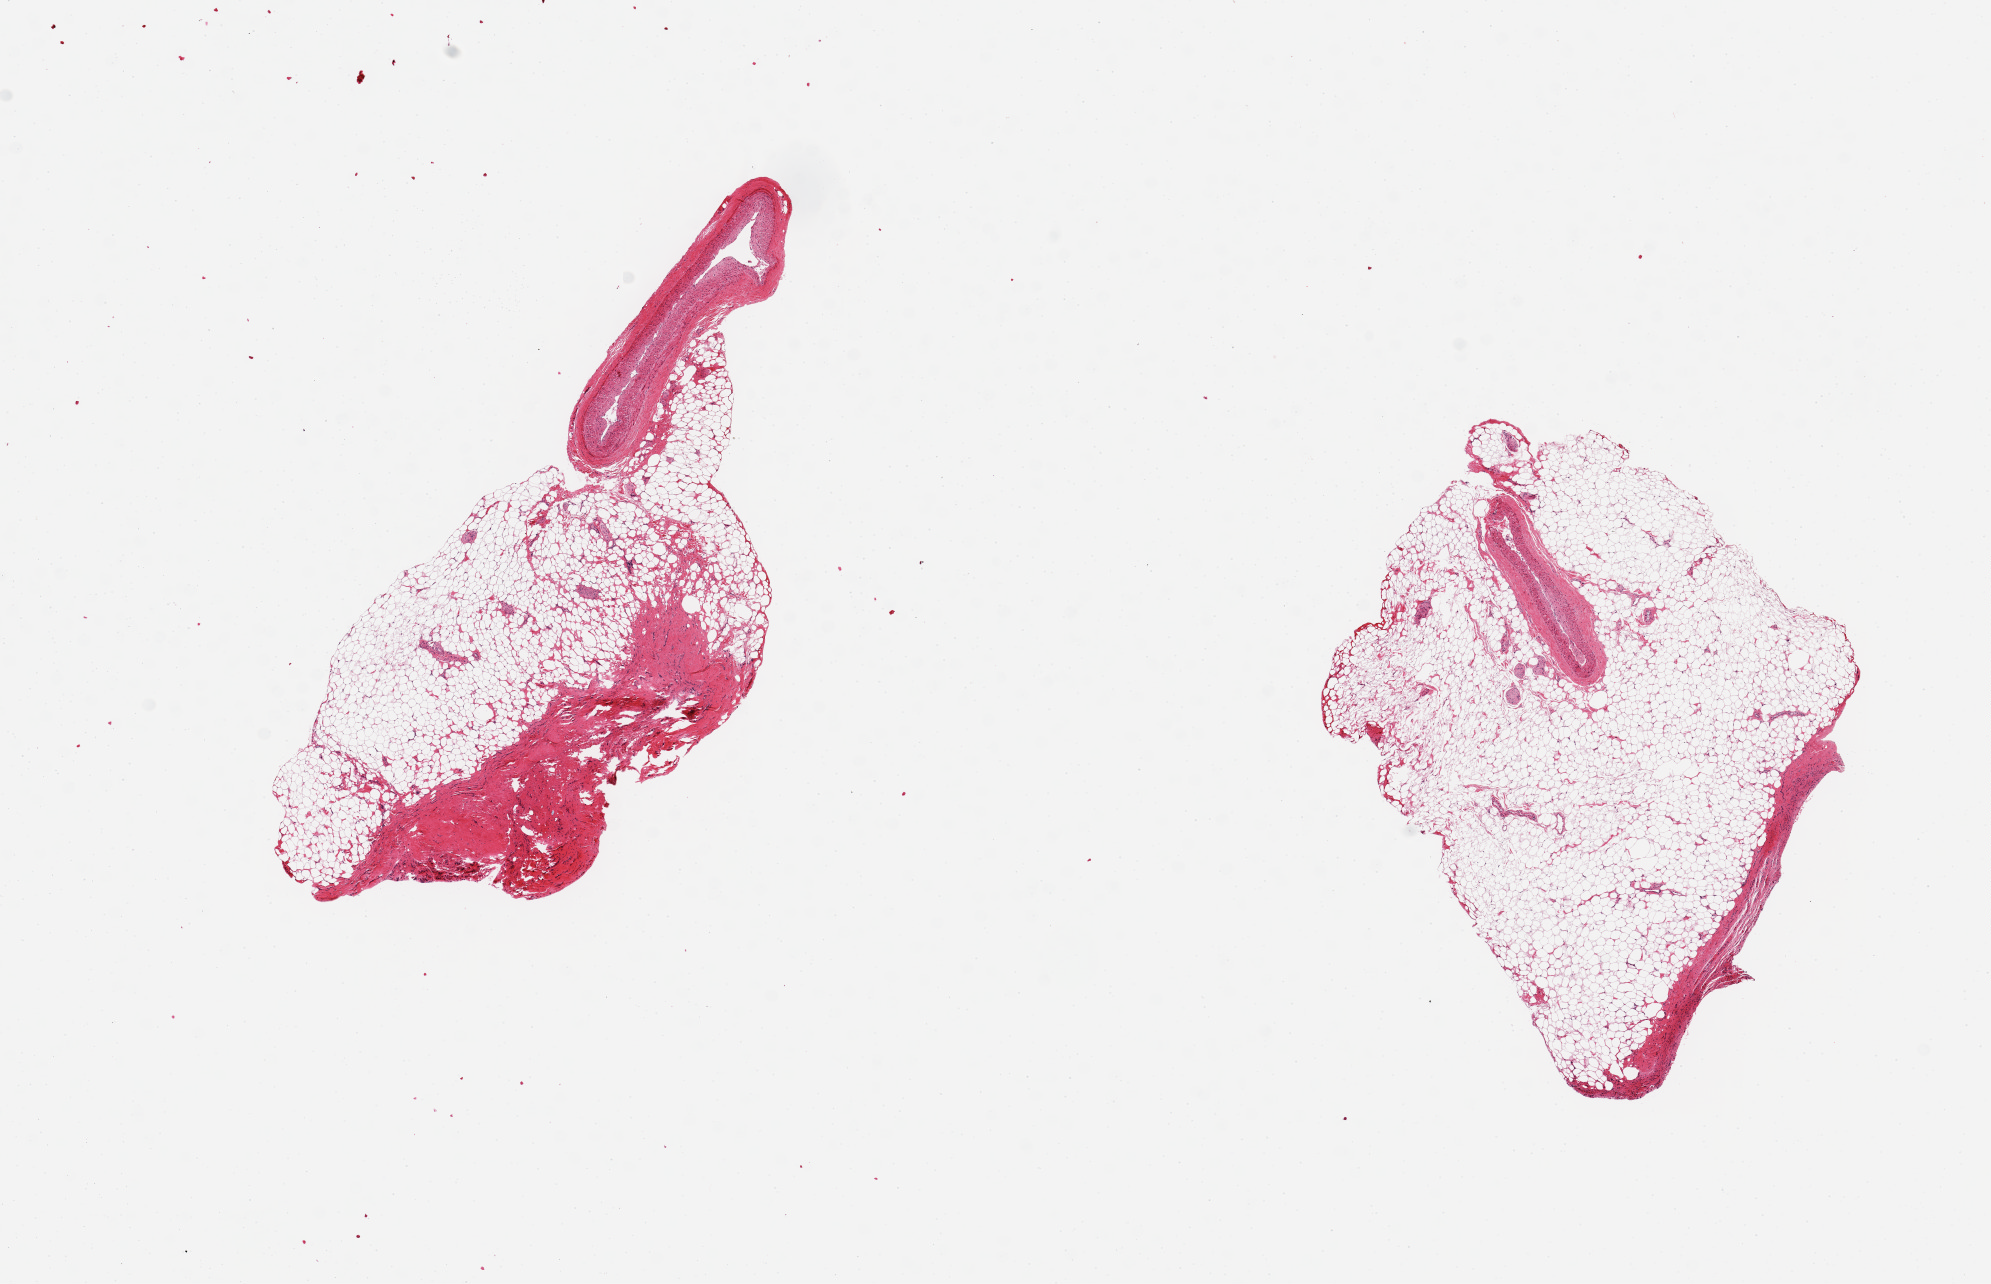
Digitized H&E-stained section, shown as a low-resolution overview of the whole scanned area (about 15.8 x 10.2 mm, from a 20x scan). PAXgene-fixed paraffin-embedded (PFPE) section. Section of coronary artery (target tissue). Donor tissue sample.
Reviewer comment on this tissue sample: 2 pieces 6.6x2.6 & 4x4 mm; large amount of adjacent adipose, >60%; artery is 2.7x0.5 and 1.6x0.5 mm.